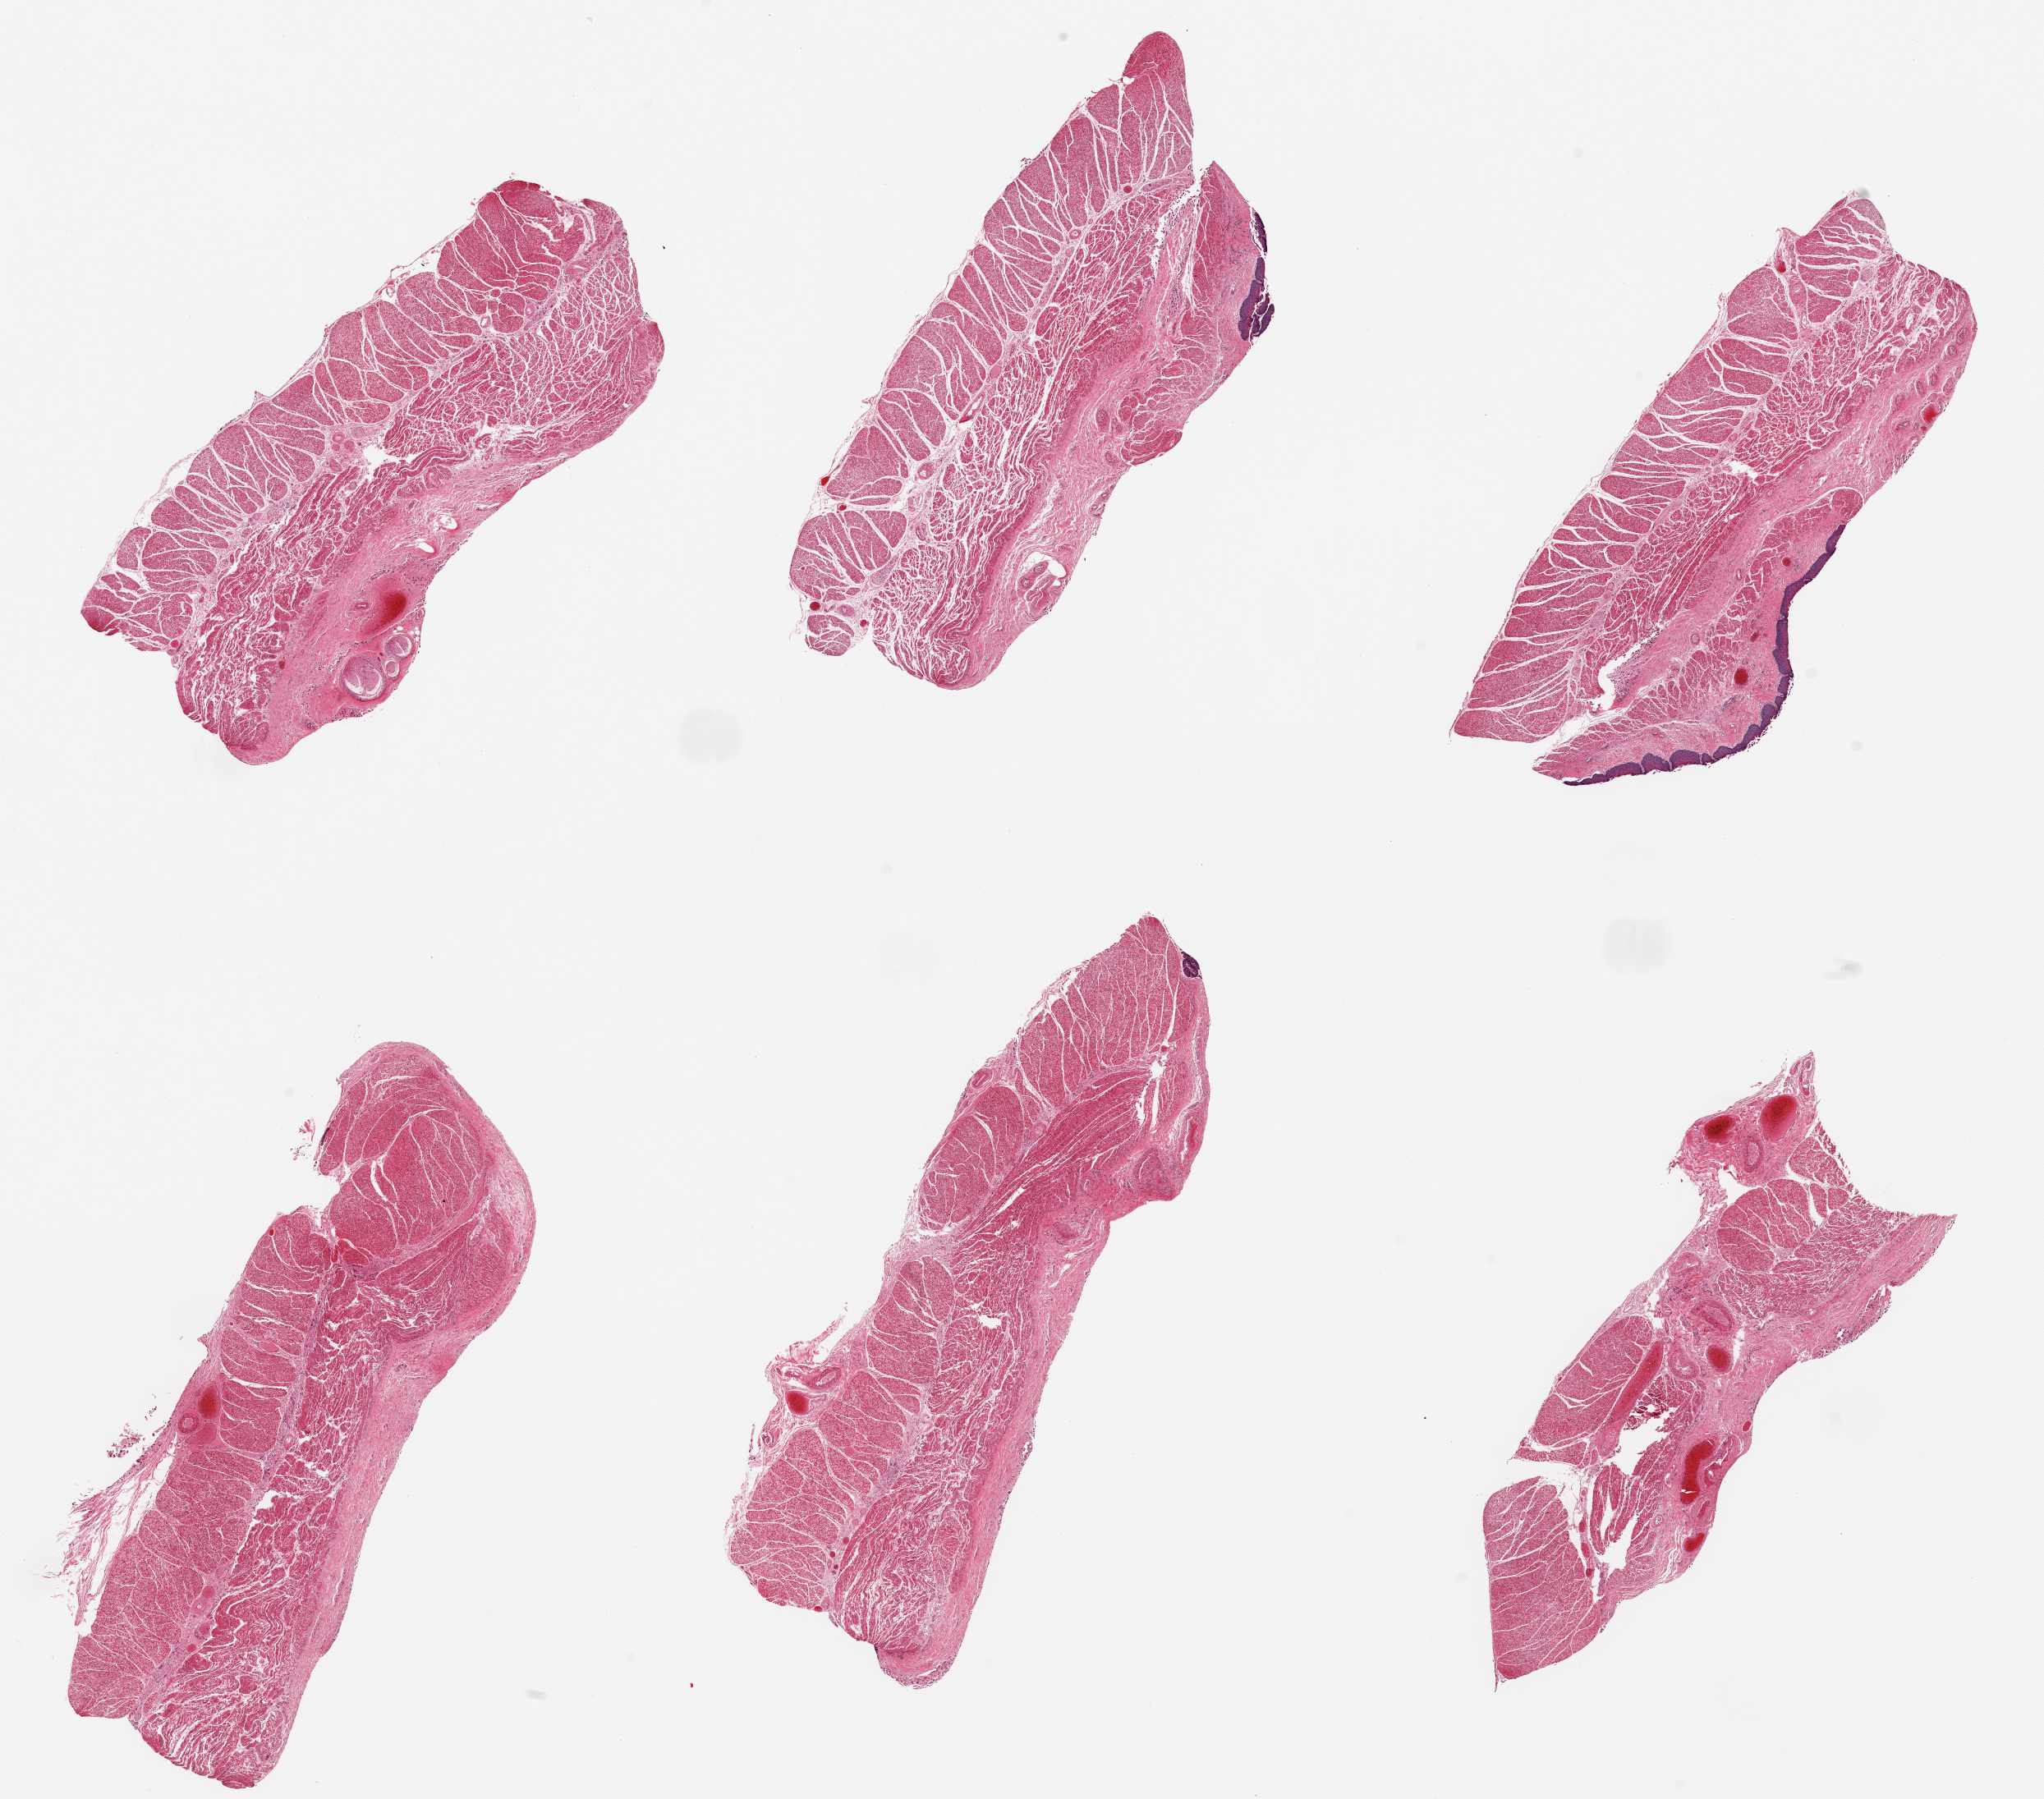
Hematoxylin and eosin (H&E) whole-slide image, brightfield, a low-resolution overview of the entire scanned area, about 19.7 x 17.3 mm, PAXgene-fixed, paraffin-embedded tissue, sampled site (target tissue): esophageal muscle, donor tissue sample. Donor: female.
Pathologist's review note for this sample: 6 pieces, target muscularis, trace adherent squamous mucosa, <5%.